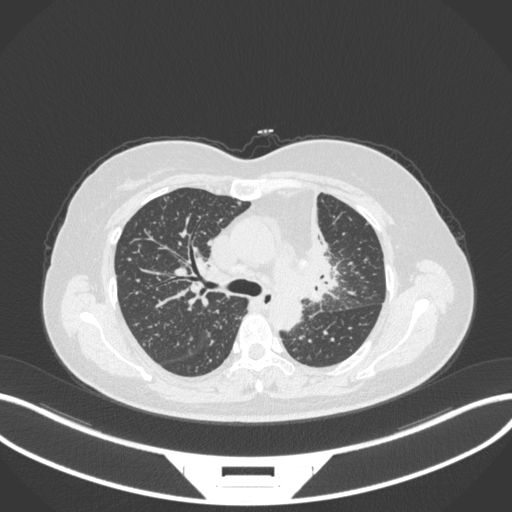
Chest CT, one axial slice; position 221 of 348 along the scan axis; reconstruction kernel B31f; lung window (W 1500 / L -600 HU); 1 mm slice thickness; 512 × 512 image matrix, field of view 400 × 400 mm. Female patient, age 49 years. Case-level facts recorded for this patient, not image findings: clinical TNM (as recorded): T1c N0 M1.
Structures marked on this image (rectangle marked by the reading radiologist):
- lung tumour (recorded histology: adenocarcinoma): bounding box <298,189,341,308> (left, top, right, bottom; pixels)